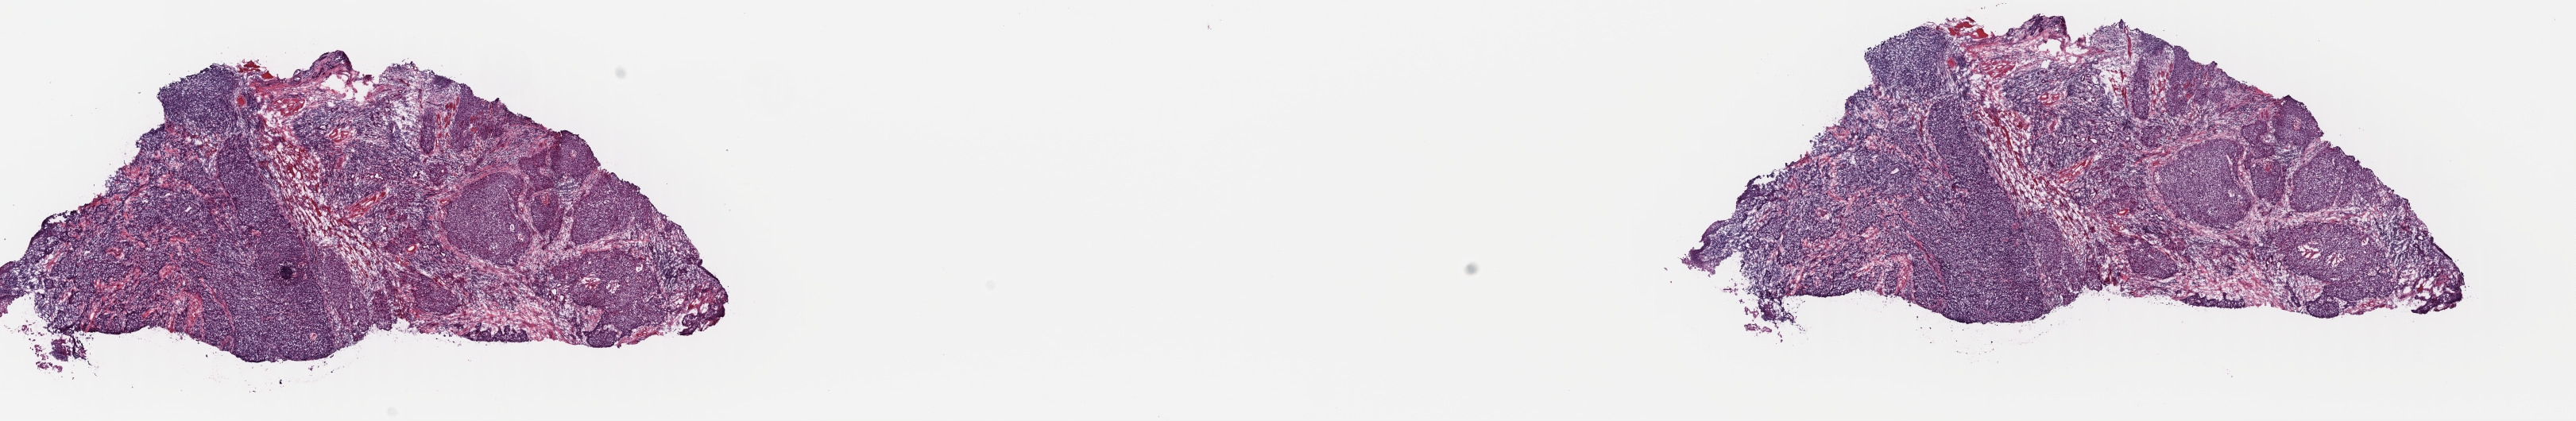
Hematoxylin and eosin (H&E) stained whole-slide image — whole scanned area (about 25.5 x 4.2 mm, from a 40x scan) shown as a low-resolution overview, frozen section, sample: primary tumour, head and neck. Patient: male, age at initial diagnosis 59 years. Histologic grade: GX (grade cannot be assessed). Composition of this section per pathologist review: tumour cells 70%, tumour nuclei 80%, normal cells 10%, stromal cells 20%, necrosis 0%. Inflammatory infiltration, as recorded: lymphocyte infiltration 0%, monocyte infiltration 0%, neutrophil infiltration 0%.
Histologic diagnosis: Squamous cell carcinoma, large cell, nonkeratinizing, NOS (base of tongue, NOS). AJCC pathologic stage: IVA (7th edition).